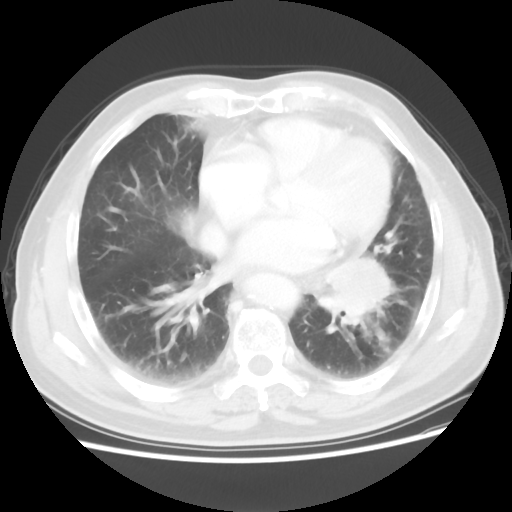
Chest CT, one axial slice; slice 25 of 56 in the series (ordered by position); lung window (W 1500 / L -600 HU); 5 mm slice thickness; 512 × 512 image matrix. Male patient, age 75 years. Case-level facts recorded for this patient, not image findings: clinical TNM (as recorded): T3 N0 M0.
Outlined on this slice (bounding box drawn by a radiologist):
- lung tumour (recorded histology: squamous cell carcinoma): box from (x=317, y=250) to (x=405, y=320) px